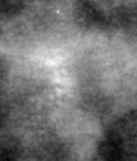
Crop from a digitized film mammogram around one marked abnormality, left breast, MLO view, BI-RADS breast density category 4 (scale 1–4).
- Marked abnormality: calcifications, morphology pleomorphic, distribution clustered; BI-RADS assessment category 4; subtlety rating 1 on a 1 (subtle) to 5 (obvious) scale; pathology result (as recorded, not read from the image): benign.